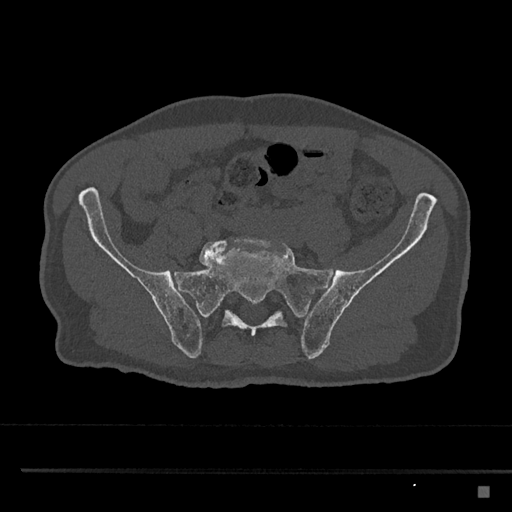
CT including the spine, one axial slice. Position 528 of 797 along the scan axis. 120 kVp. Bone window (W 1800 / L 400 HU). 0.5 mm slice thickness. 512 × 512 image matrix, field of view 391 × 391 mm. Patient: male, 59 years. Case-level facts recorded for this patient, not image findings: primary cancer: prostate.
Annotated regions visible in this slice (semi-automatically segmented with operator editing):
- L5 vertebra: bounding box <199,237,271,267> (left, top, right, bottom; pixels)